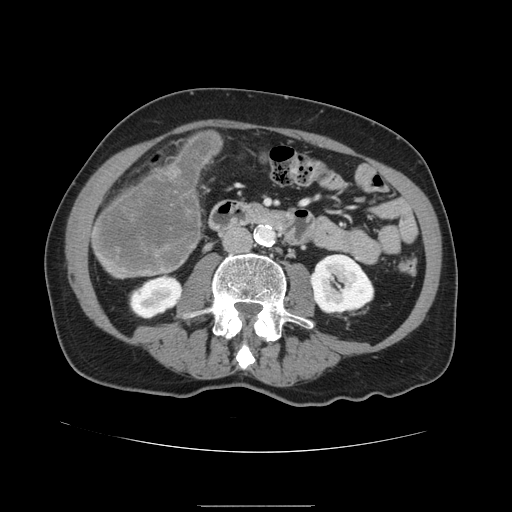
Contrast-enhanced abdominal CT, one axial slice; slice 33 of 168 in the series (ordered by position); 120 kVp; intravenous contrast given; soft-tissue window (W 400 / L 40 HU); 512 × 512 image matrix. Male patient, age 74 years. From the clinical record (not read from this slice): diagnosis: colorectal cancer liver metastases, imaged before liver resection; multiple liver metastases: no; largest metastasis: 14.5 cm; chemotherapy before resection: no.
Annotated regions visible in this slice (outlined manually by an expert reader):
- liver: bounding box [x1, y1, x2, y2] px = [91, 131, 223, 279]
- liver metastasis: [95, 134, 219, 274]